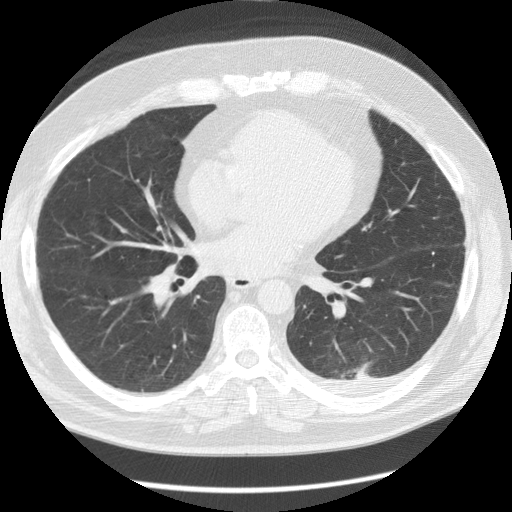
Low-dose screening chest CT, one axial slice. Slice 60 of 126 in the series (ordered by position). Reconstruction kernel STANDARD. 120 kVp. Lung window (W 1500 / L -600 HU). 2.5 mm slice thickness. 512 × 512 image matrix, field of view 370 × 370 mm.
Outlined on this slice (expert manual segmentation):
- lesion 1 (tumor, lower lobe of left lung): box from (x=355, y=361) to (x=373, y=377) px